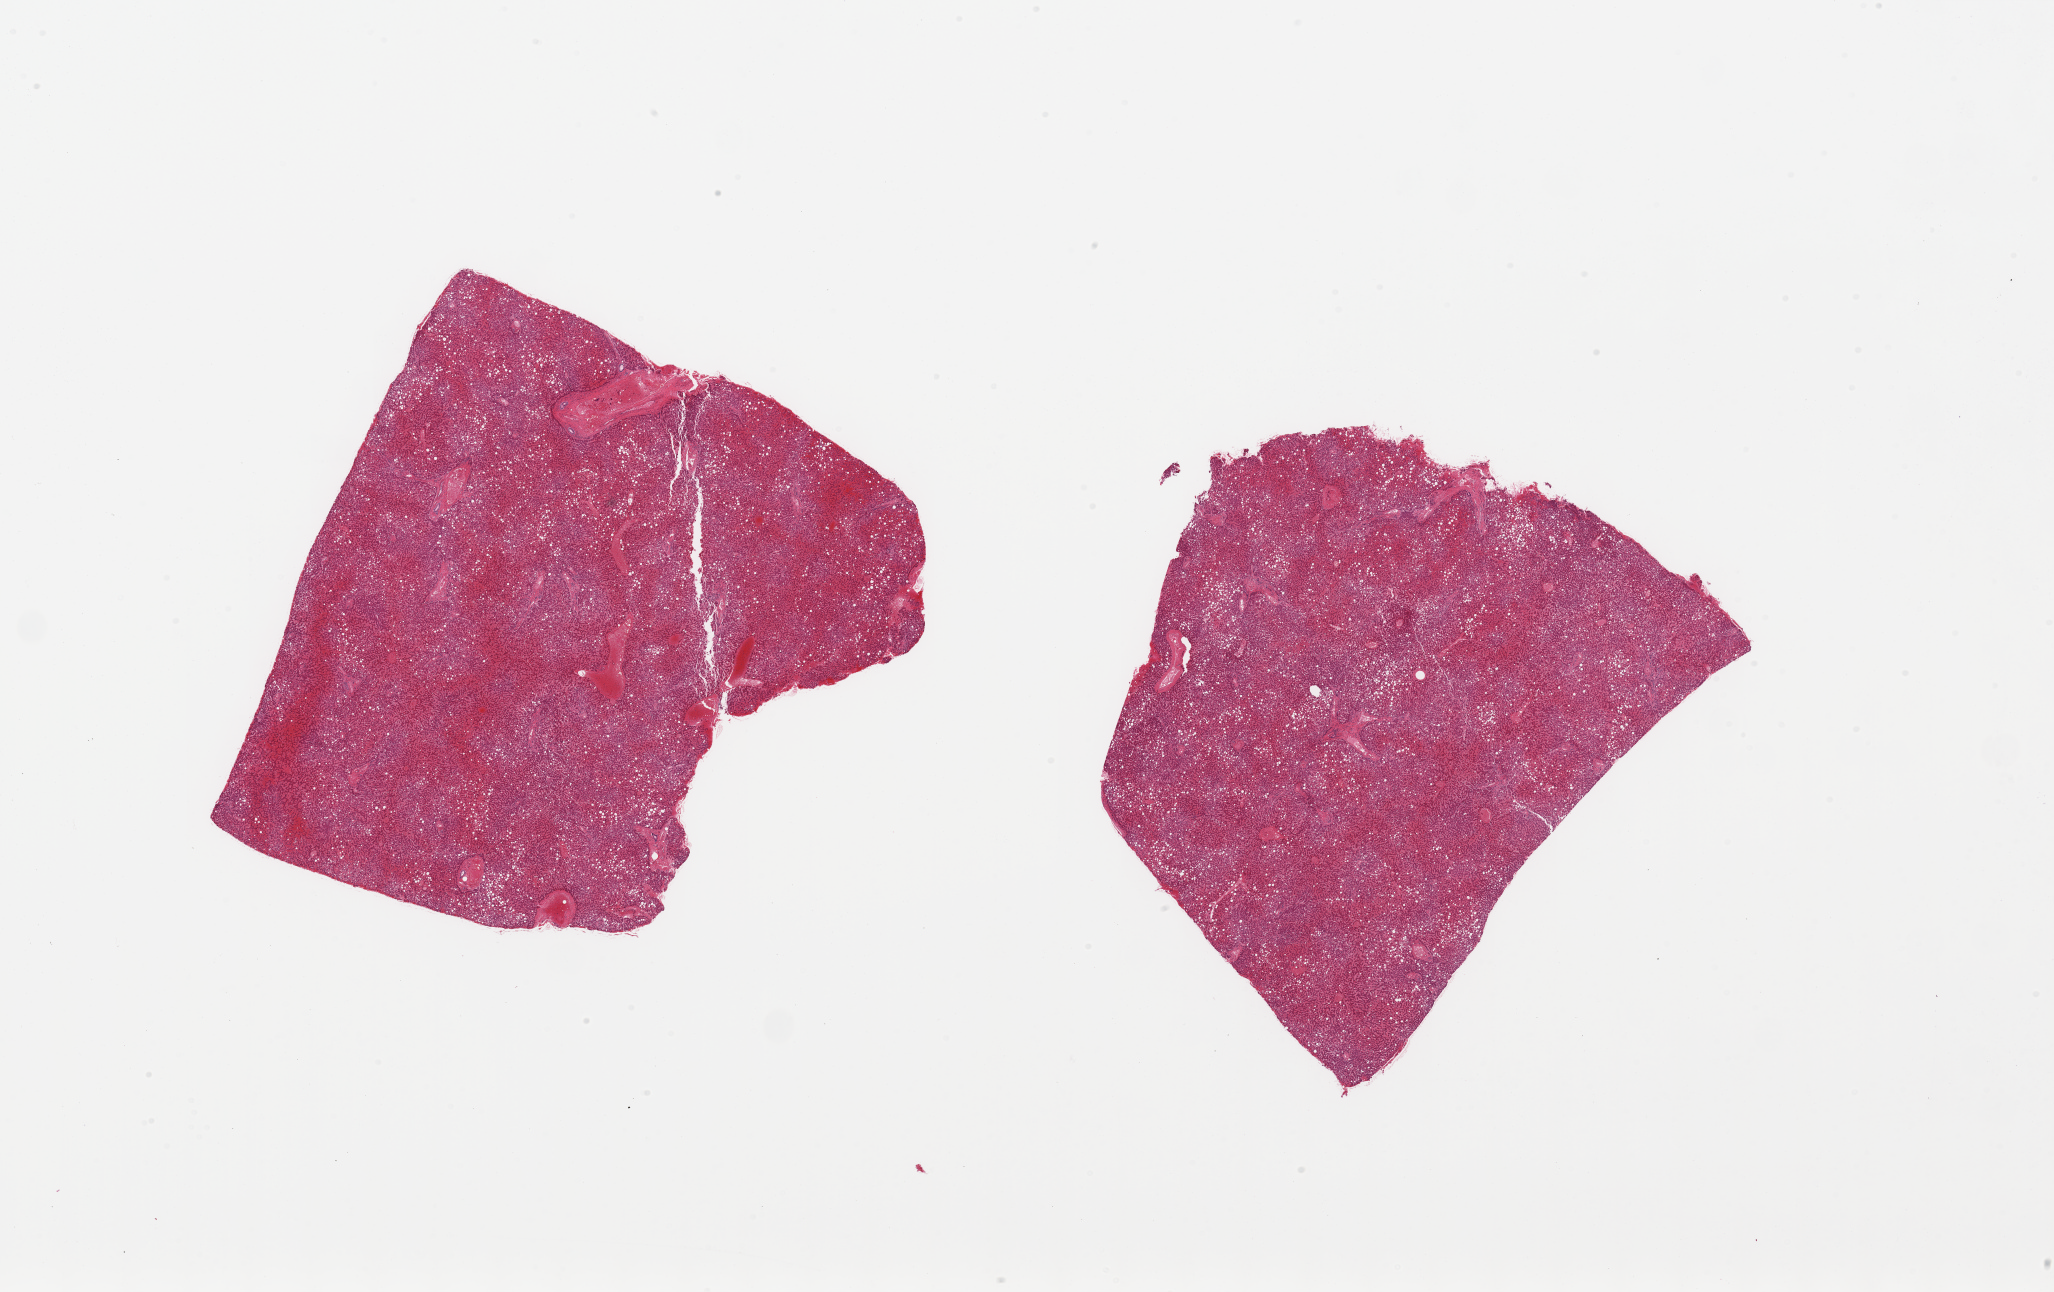
Digitized haematoxylin and eosin-stained section, brightfield, low-resolution overview of the scanned area, about 32.5 x 20.4 mm; PAXgene-fixed paraffin-embedded (PFPE) section; target tissue: liver; donor tissue sample. Donor sex: male.
Pathologist's review note for this sample: 2 pieces, marked passive congestion; moderate macrovesicular steatosis ( 40-50% of parenchyma).